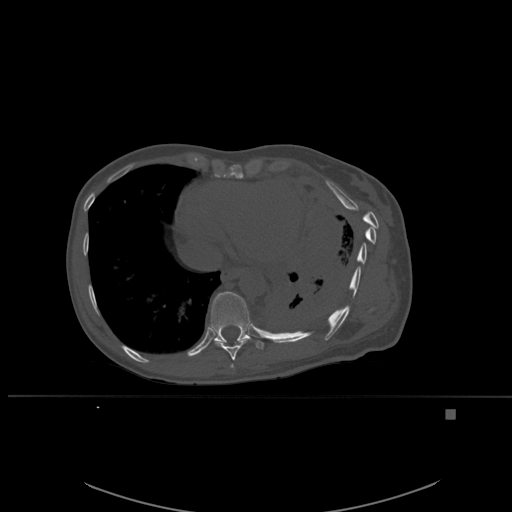
CT including the spine, one axial slice. Slice 326 of 537 in the series (ordered by position). Bone window (W 1800 / L 400 HU). 1.5 mm slice thickness. 512 × 512 image matrix. Female patient, age 45 years. Case-level facts recorded for this patient, not image findings: primary cancer: lung.
Structures marked on this image (semi-automatic segmentation, software-assisted and operator-edited):
- T10 vertebra: bounding box (x1, y1, x2, y2) in pixels: (206, 291, 264, 350)
- T8 vertebra: (230, 364, 234, 368)
- T9 vertebra: (214, 339, 248, 361)